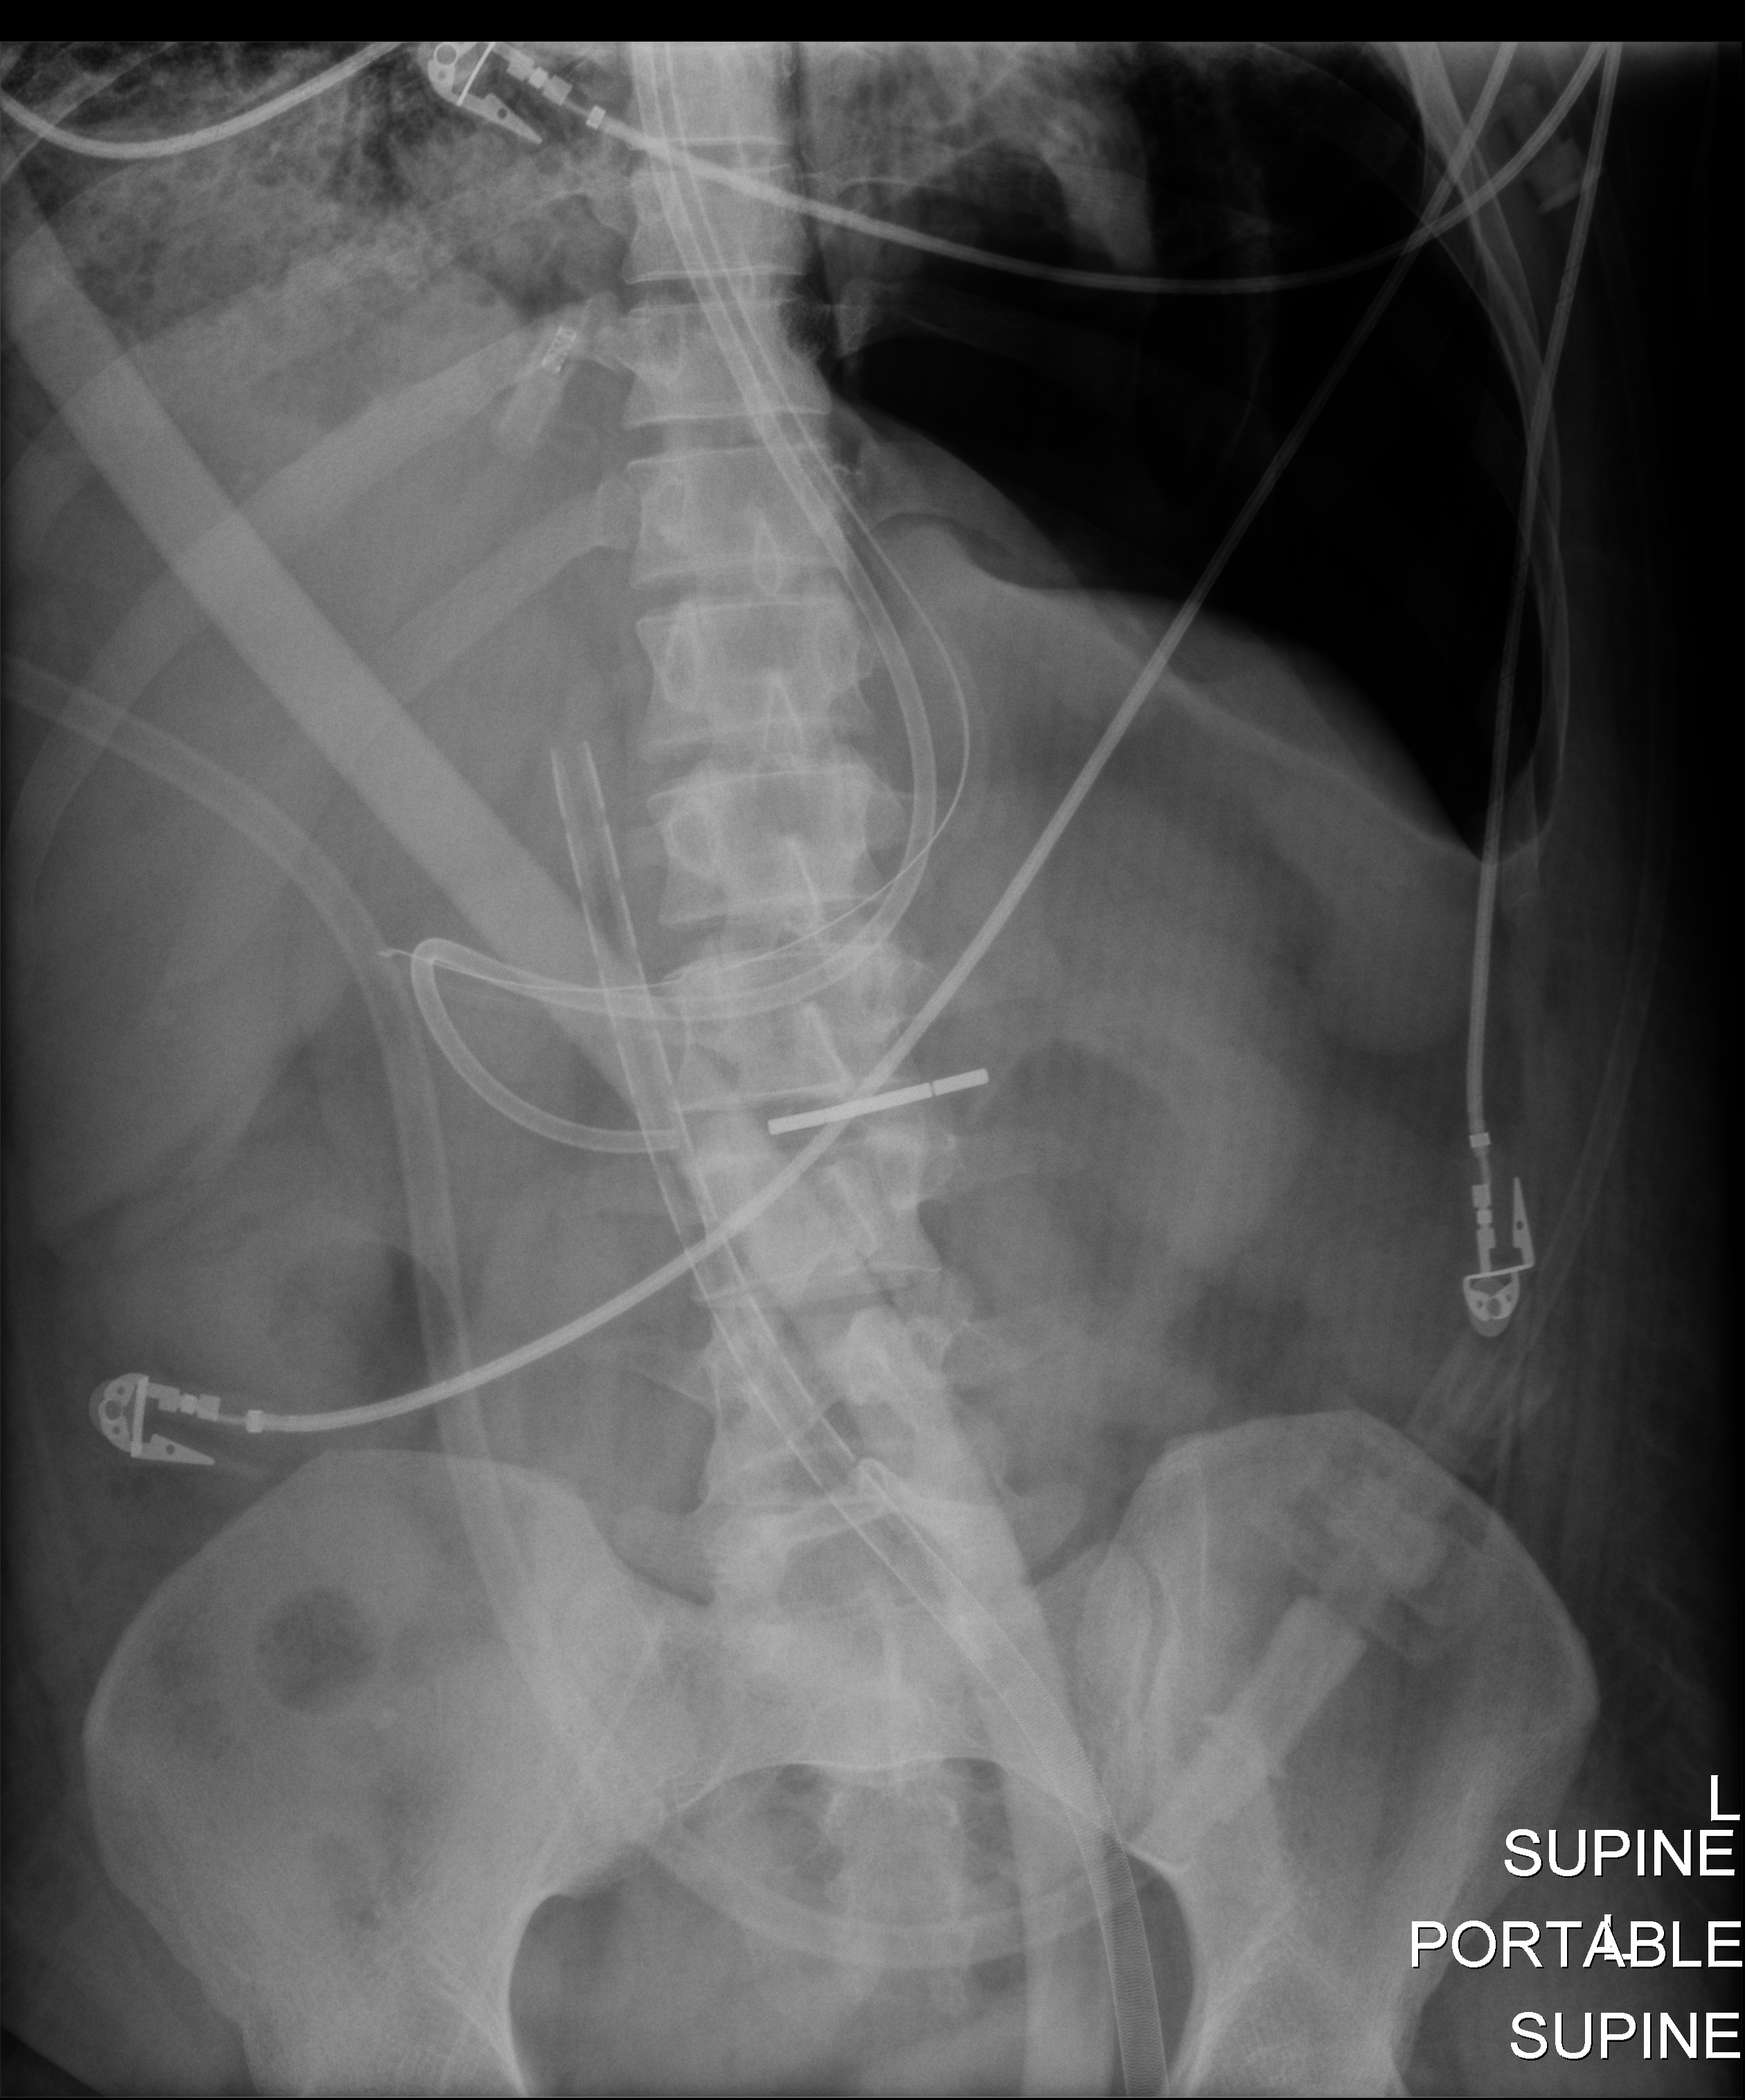
Bedside abdomen radiograph (digital radiography), anteroposterior (AP) projection. Adult patient hospitalised with COVID-19, age 18–59 years.
Admission-level facts for this patient (not findings on this image; timing relative to this image not recorded): hypertension (admission record): no; admitted to intensive care during this hospital stay: yes; mechanically ventilated during this hospital stay: yes.